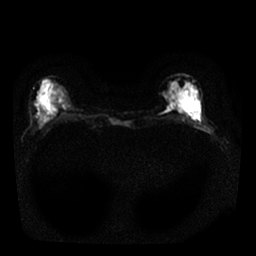
Breast MRI, one axial slice. Position 8 of 25 along the scan axis. Diffusion-weighted series; image 2 of 4 stored at this slice position (different b-values; order by instance number). 1.5 T. 256 × 256 image matrix. Female patient.
Annotated regions visible in this slice (manually delineated by an expert):
- tumour on diffusion-weighted imaging: bounding box <182,95,193,111> (left, top, right, bottom; pixels)